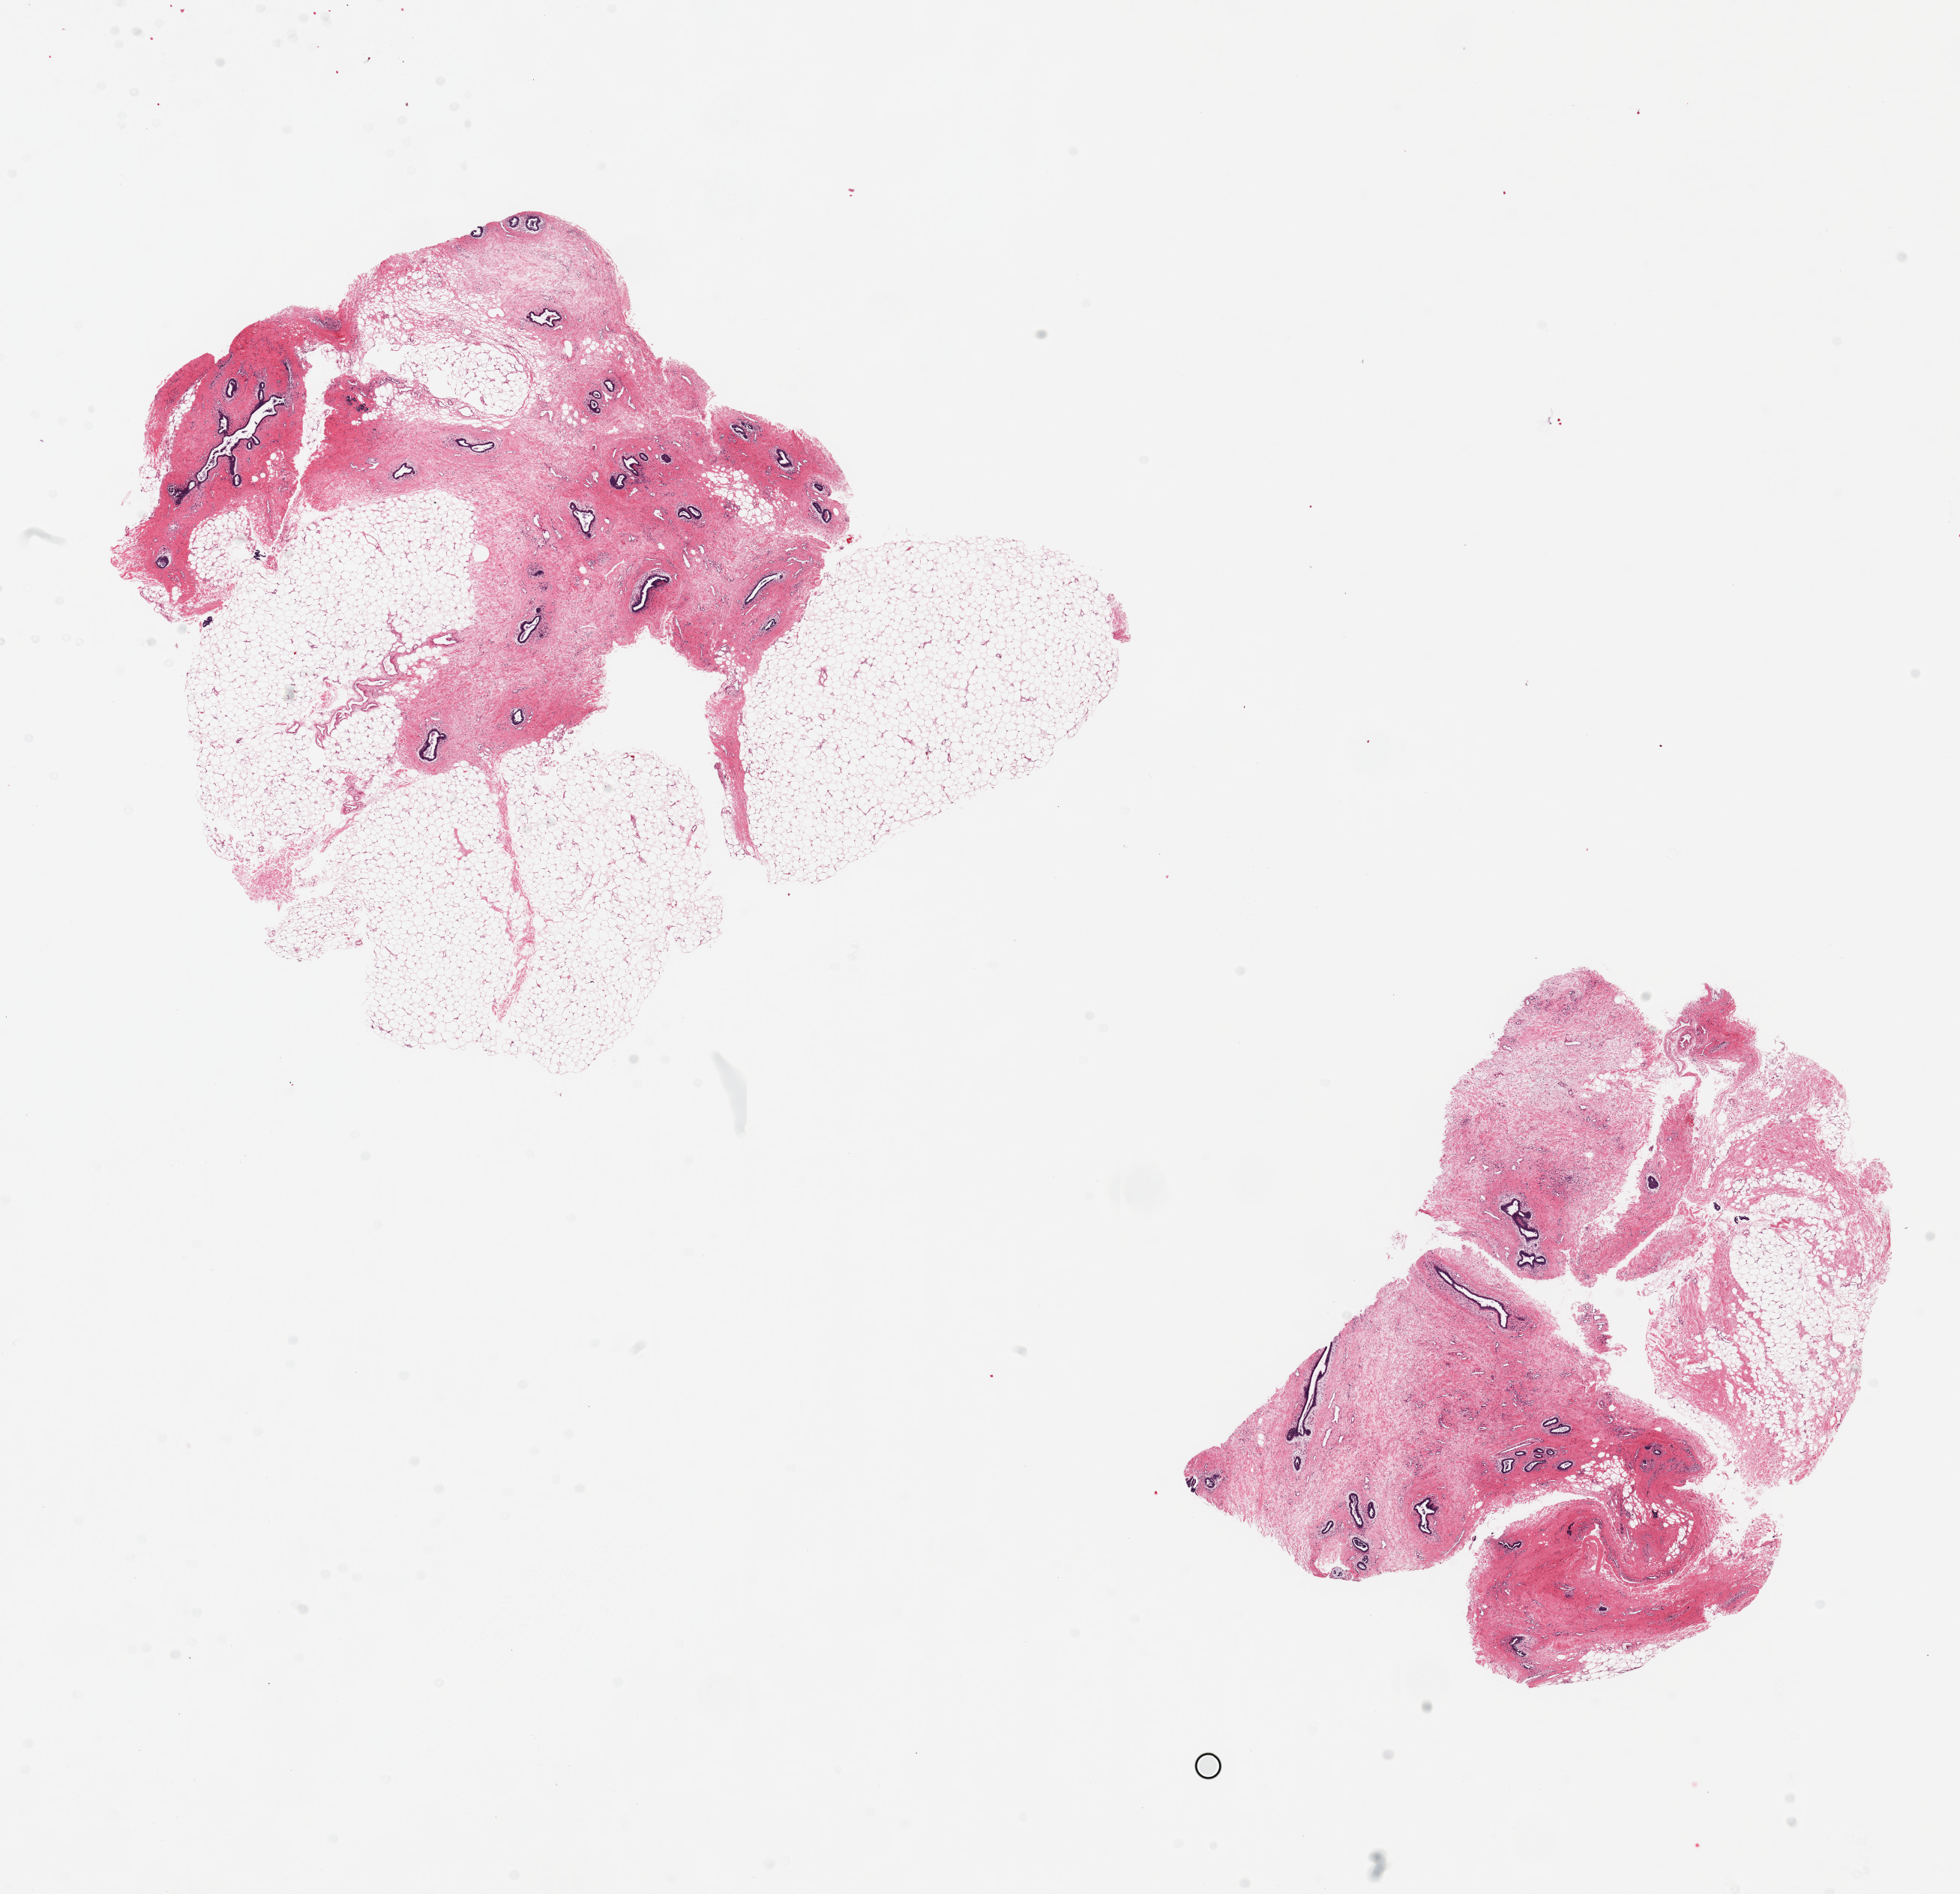
Digitized hematoxylin and eosin (H&E)-stained section, brightfield — shown as a low-resolution overview of the whole scanned area (about 20.7 x 20.0 mm, acquisition: 20x scan). PAXgene-fixed, paraffin-embedded tissue. Sampled site (target tissue): breast. Tissue donor sample. Donor sex: male.
• pathologist's review note for this sample: 2 pieces, 9x8 & 7x6mm; gynecomastia with hyalinized stroma and ductal hyperplasia